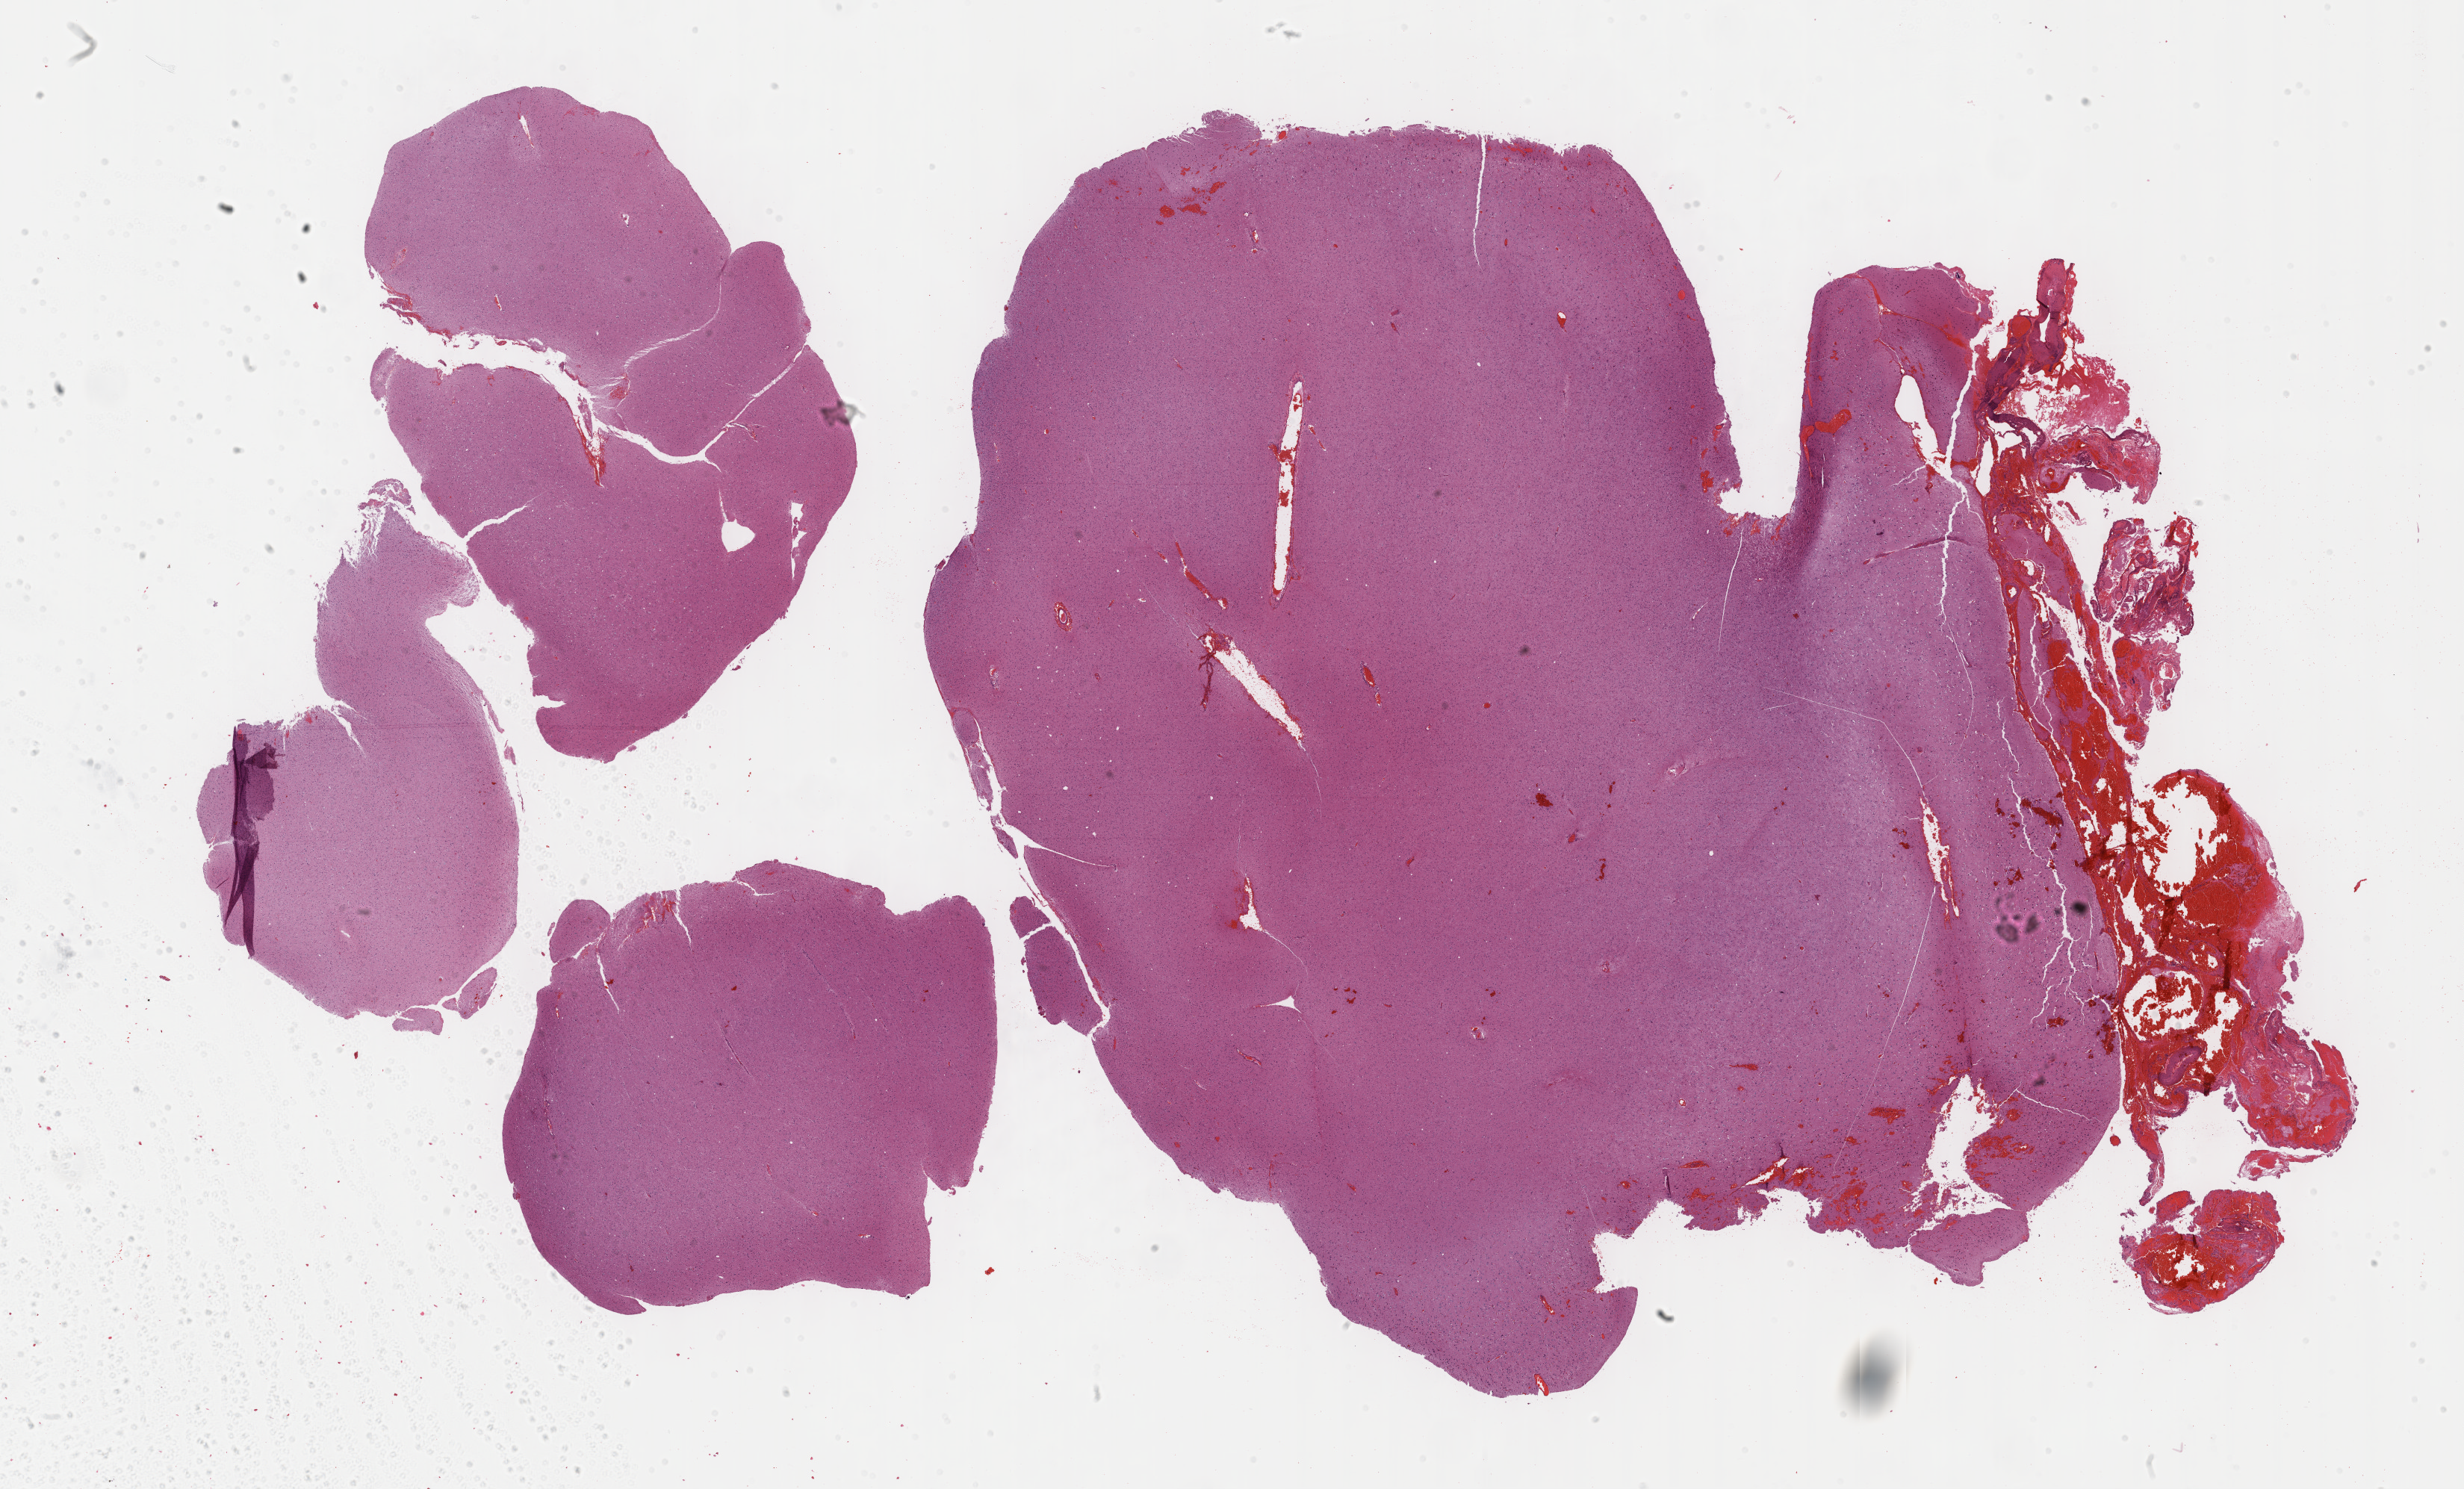
H&E-stained whole-slide image — a low-resolution overview of the entire scanned area, about 26.7 x 16.1 mm (acquisition: 40x scan), formalin-fixed paraffin-embedded (FFPE) diagnostic section, sample: primary tumour, brain. Male patient; age at initial diagnosis 21 years.
Diagnosis: Oligodendroglioma, NOS.